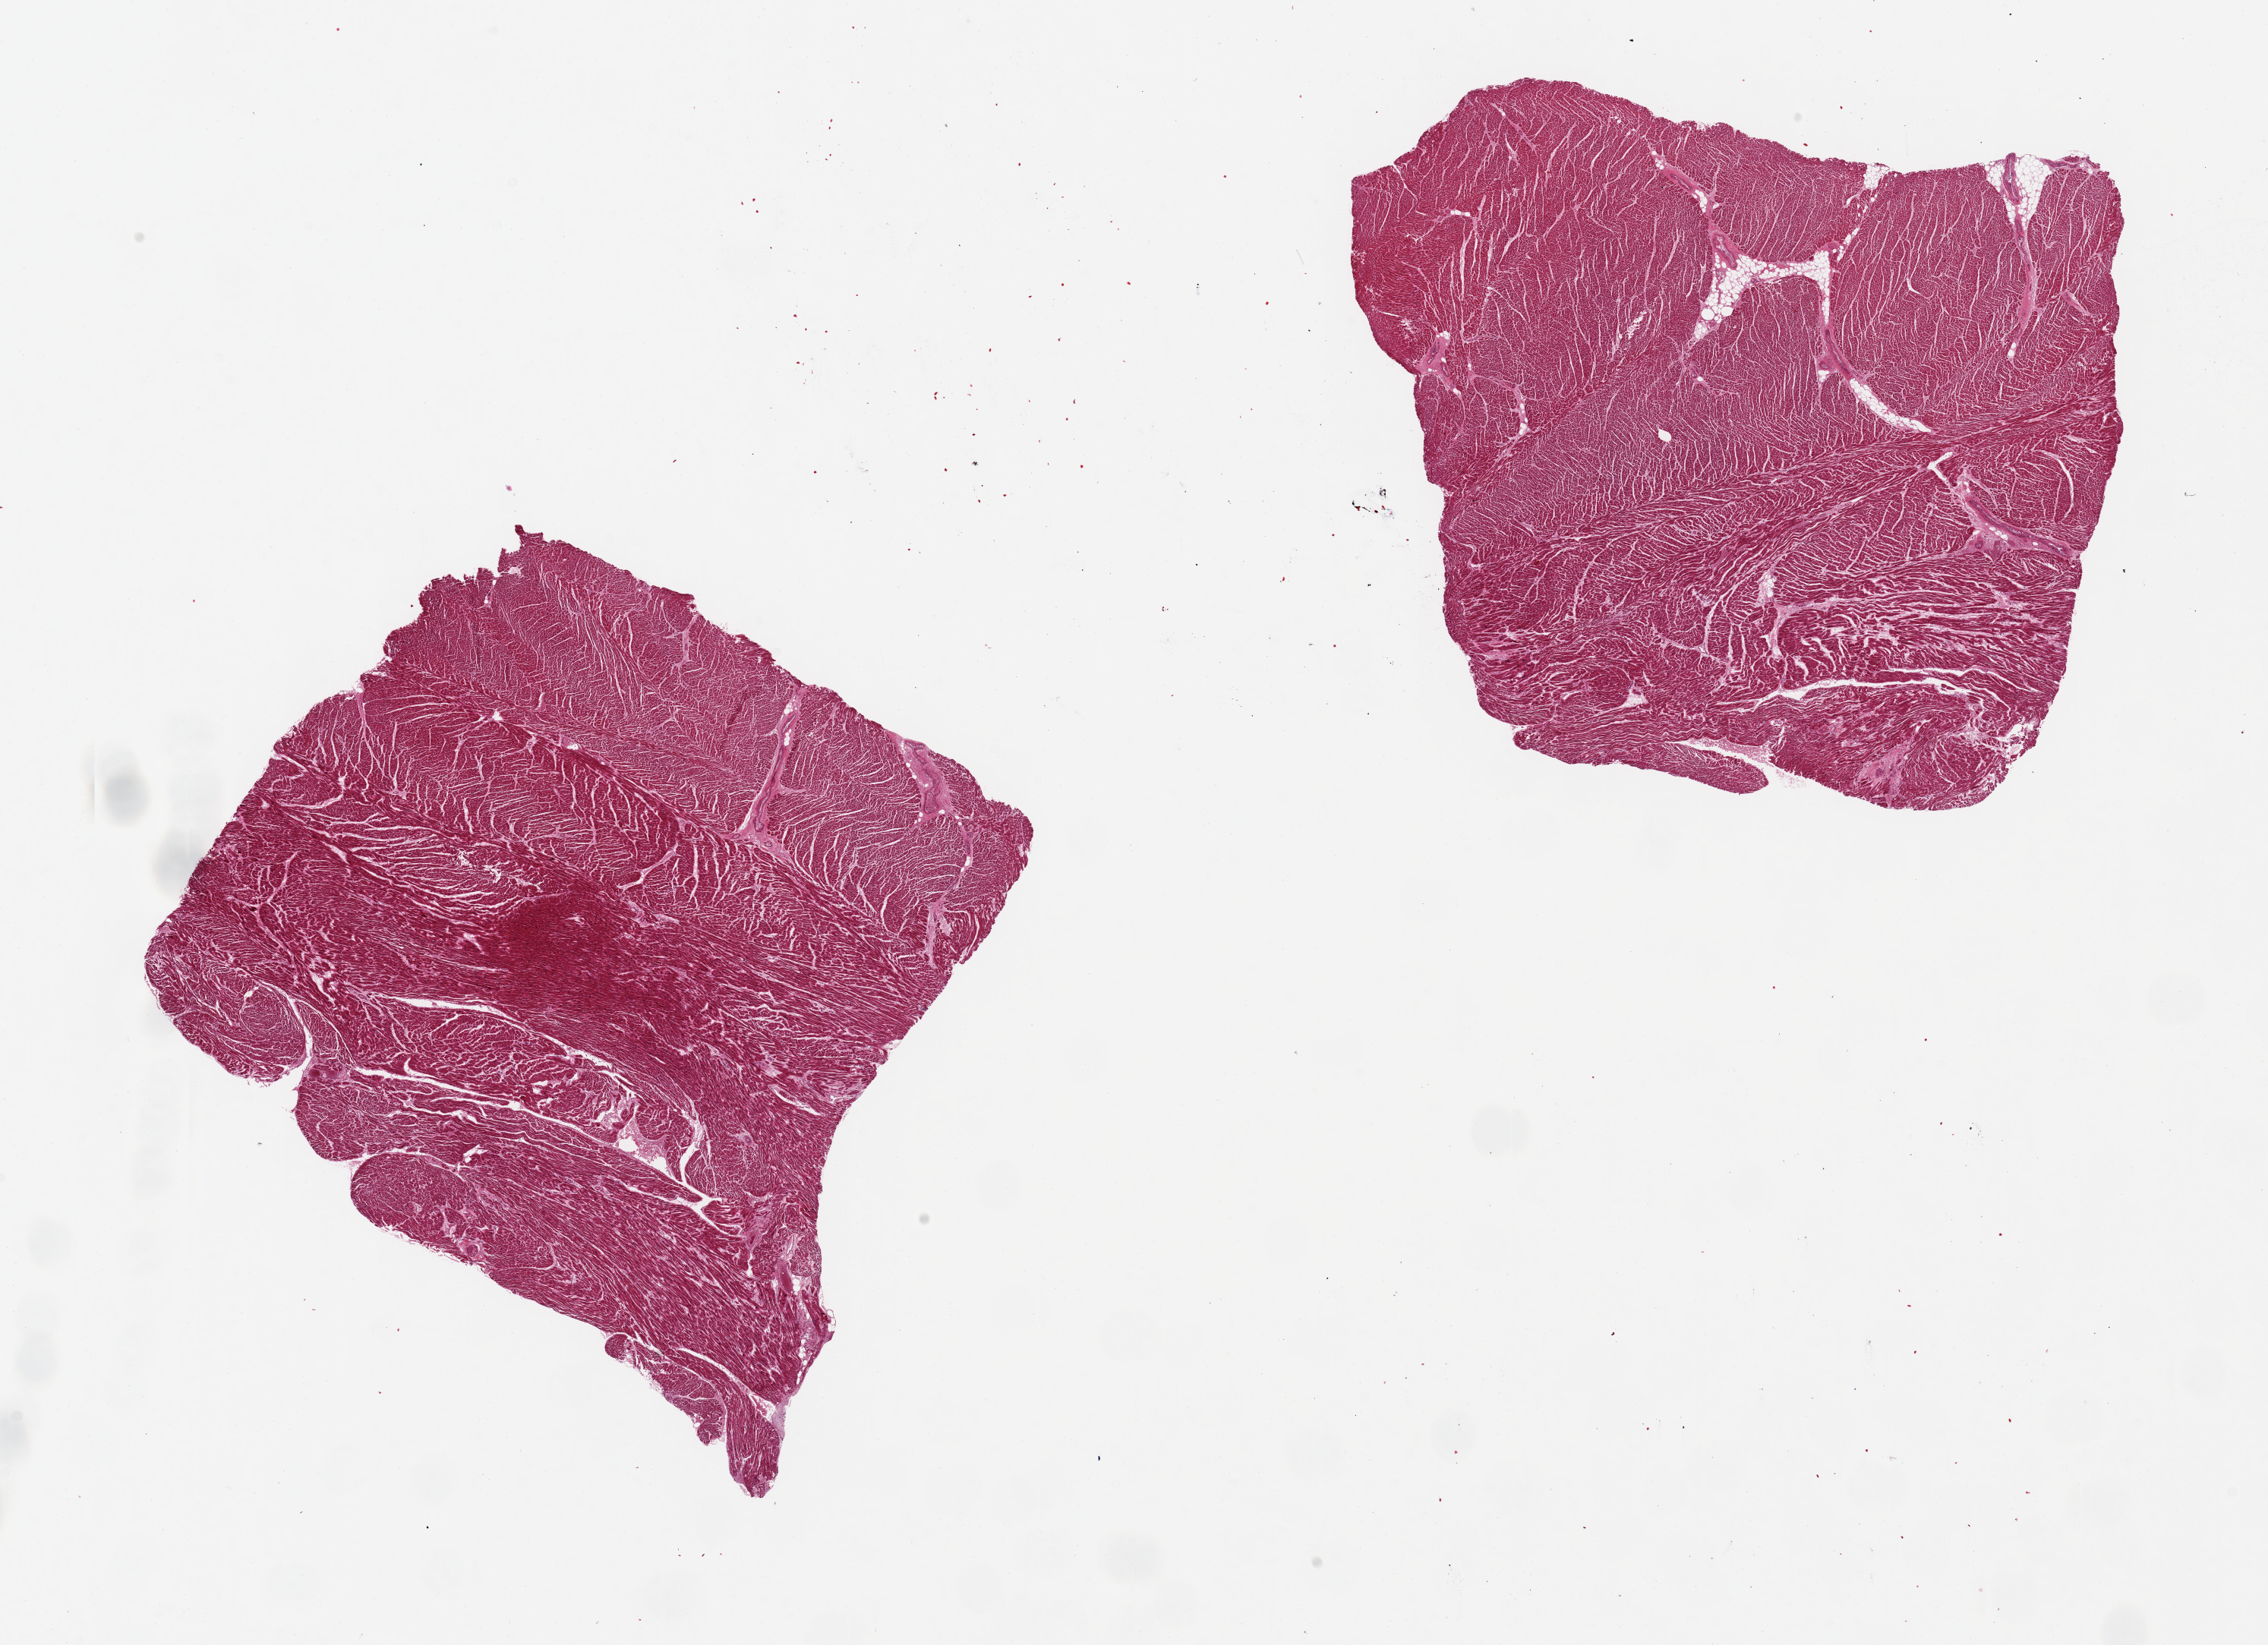
H&E whole-slide image, brightfield — shown as a low-resolution overview of the whole scanned area (about 23.6 x 17.1 mm). PAXgene-fixed paraffin-embedded (PFPE) section. Section of heart (target tissue). Donor tissue sample.
Pathologist's review note for this sample: 2 pieces, 8x7.5 & 8x7mm; central hypereosinophilic zone c/w early infarct; large nuclei c/w hypertension.